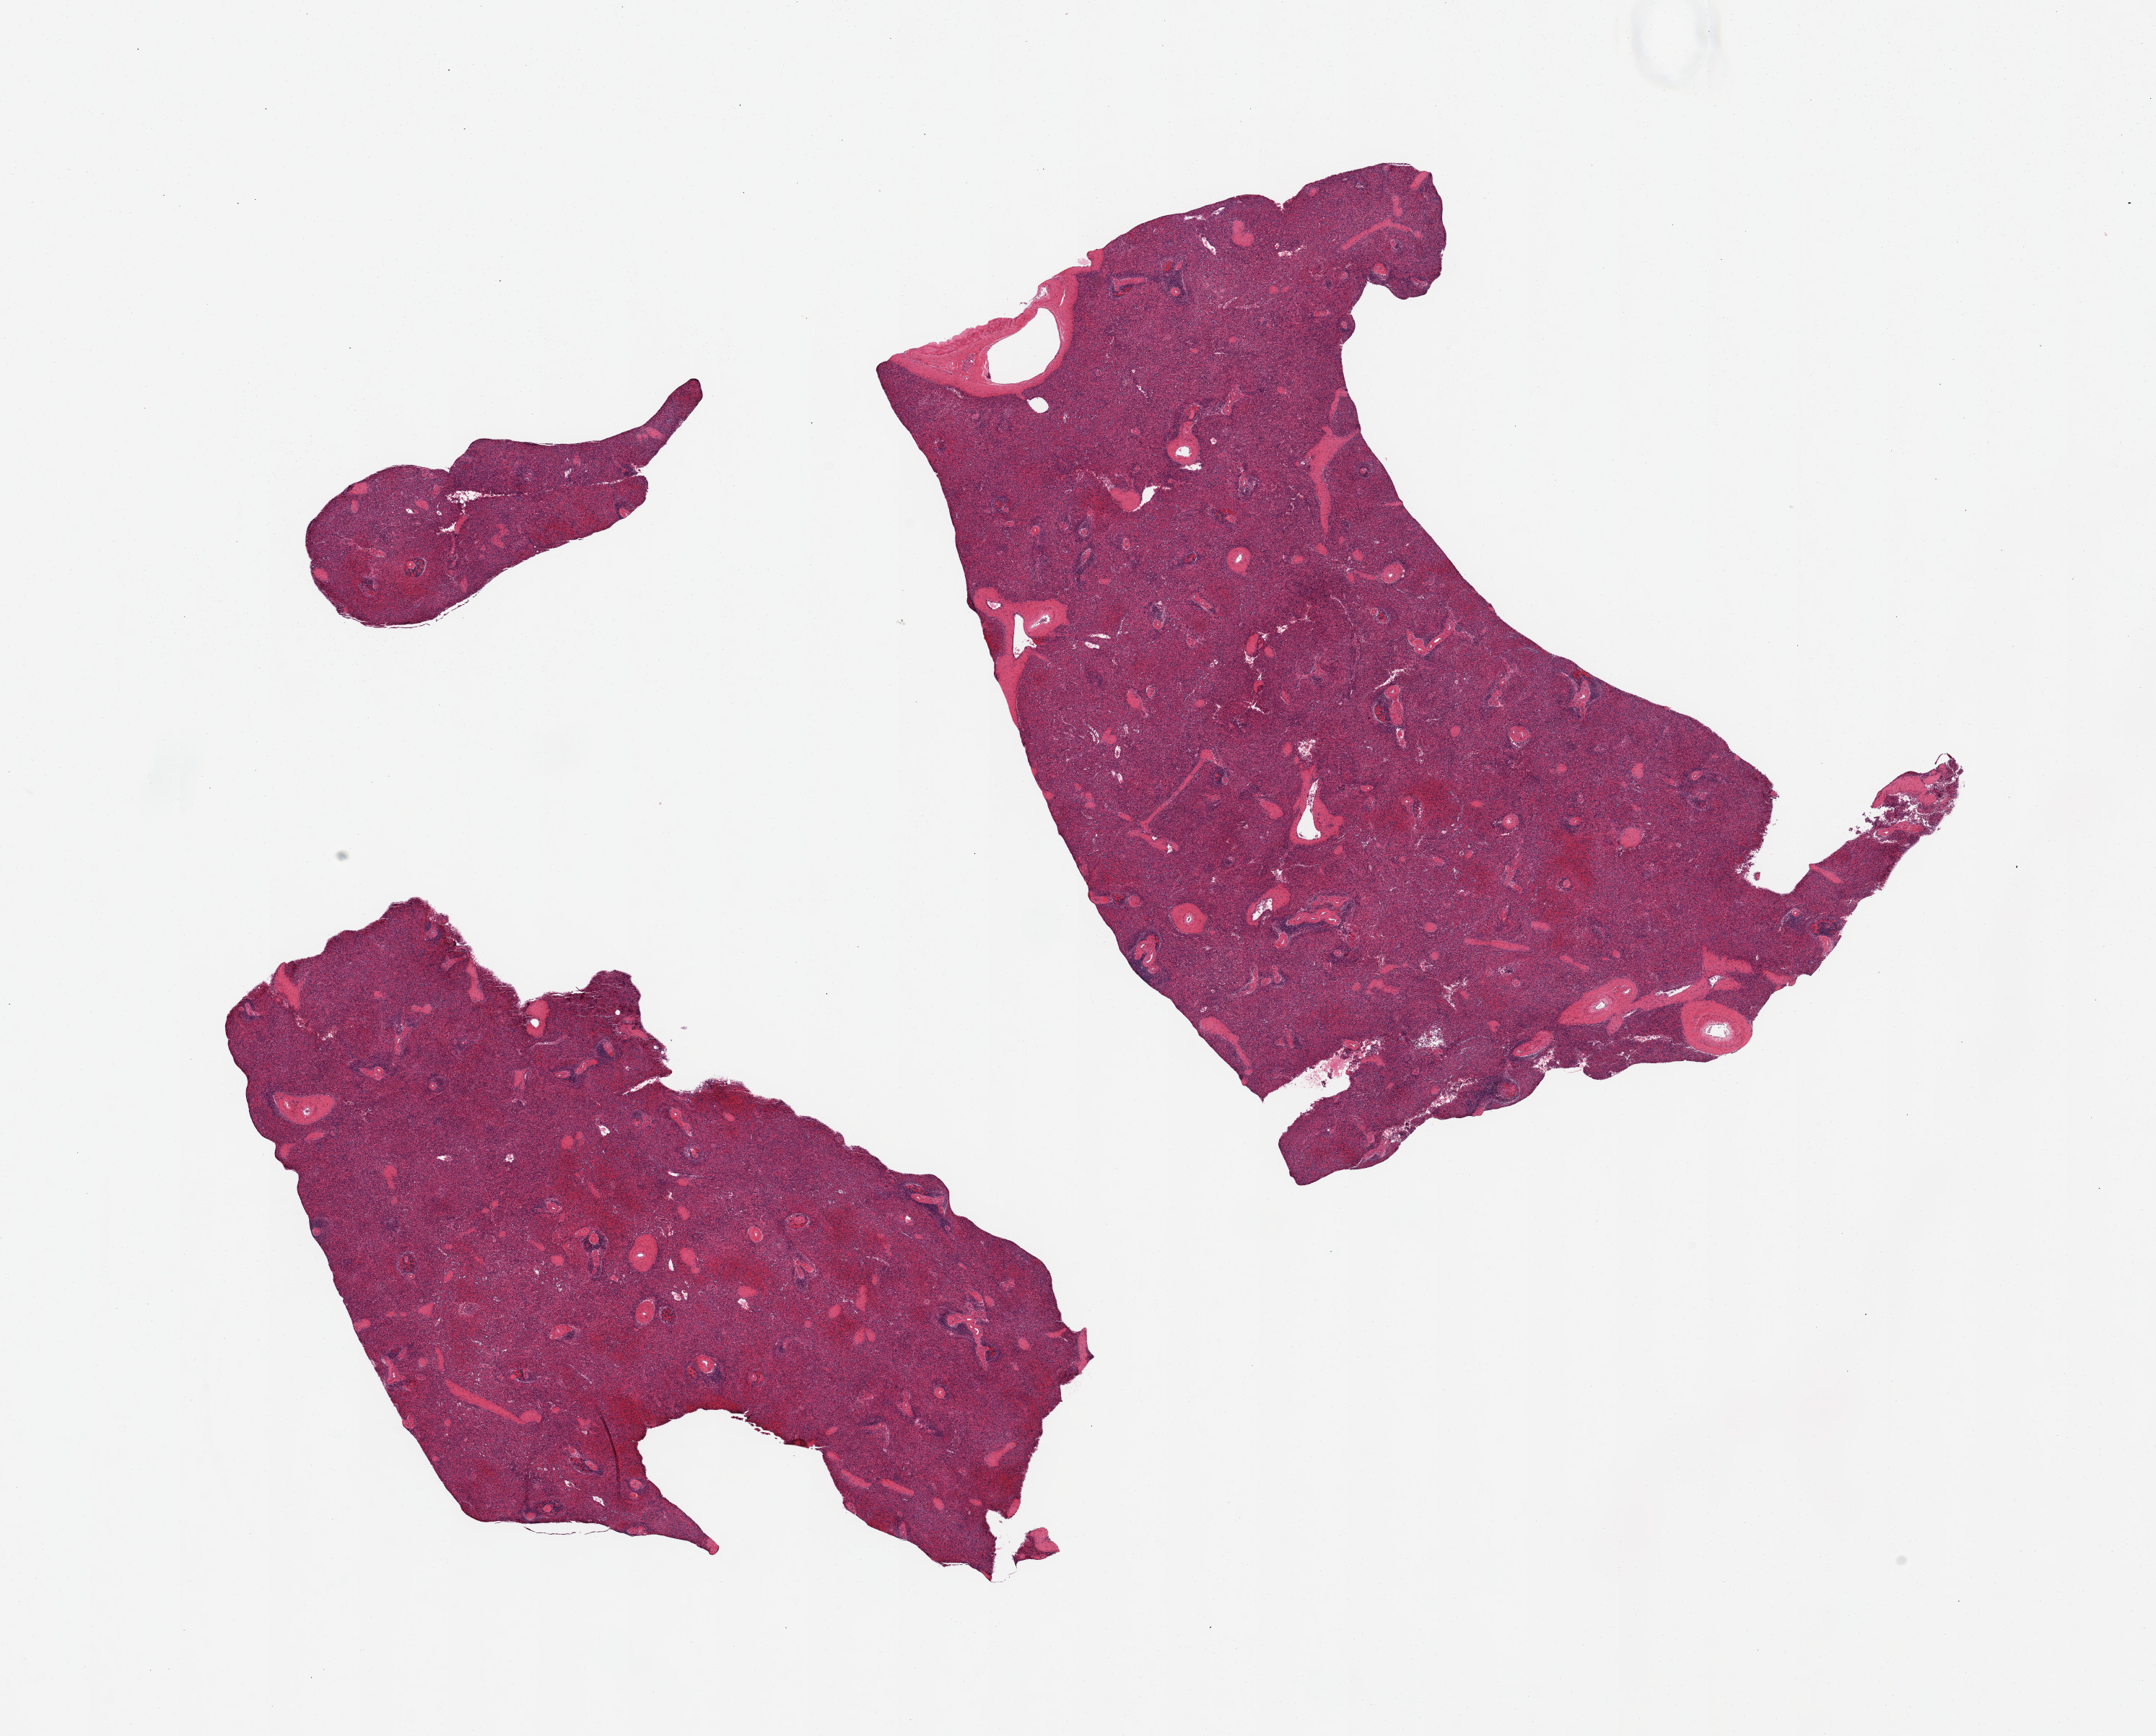
Whole-slide image, H&E stain, a low-resolution overview of the entire scanned area, about 23.6 x 19.0 mm; PAXgene-fixed paraffin-embedded (PFPE) section; sampled site (target tissue): spleen; donor tissue sample. Female donor.
Review note (as recorded): 2 pieces, minimal congestion.